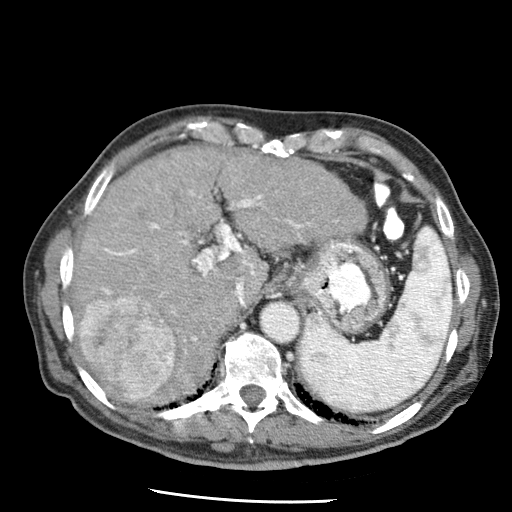
Contrast-enhanced abdominal CT (liver protocol), one axial slice. 120 kVp. Soft-tissue window (W 400 / L 40 HU). 2.5 mm slice thickness. 512 × 512 image matrix, field of view 320 × 320 mm. From the clinical record (not read from this slice): diagnosis: hepatocellular carcinoma (patient treated with transarterial chemoembolisation; whether this scan precedes or follows treatment is not stated here); TNM stage (as recorded): Stage-IIIA; Child-Pugh class: A; tumour size: 7 cm.
Annotated regions visible in this slice (semi-automatic segmentation, software-assisted and operator-edited):
- liver parenchyma outside the tumour (the mass and vessels are separate outlines, so this box may not span the whole liver): bounding box (x1, y1, x2, y2) in pixels: (70, 146, 368, 402)
- mass: (79, 293, 175, 399)
- liver vessels: (102, 190, 337, 314)